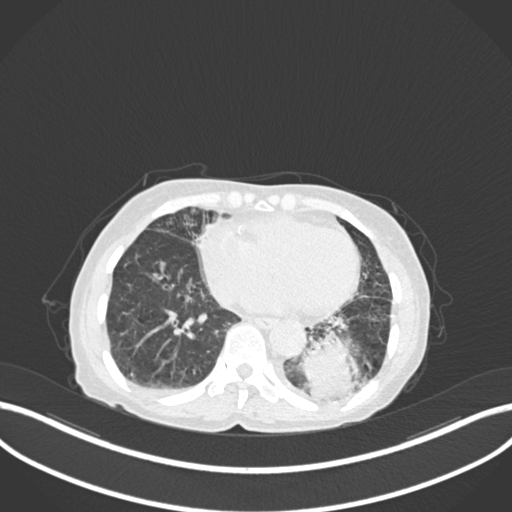
Chest CT, one axial slice. Slice 39 of 233 in the series (ordered by position). Reconstruction kernel B30f. Lung window (W 1500 / L -600 HU). 1 mm slice thickness. 512 × 512 image matrix. Female patient, age 78 years. From the clinical record (not read from this slice): clinical TNM (as recorded): T3 N0 M1.
Structures marked on this image (bounding box drawn by a radiologist):
- lung tumour (recorded histology: squamous cell carcinoma): bounding box [x1, y1, x2, y2] px = [301, 334, 369, 403]